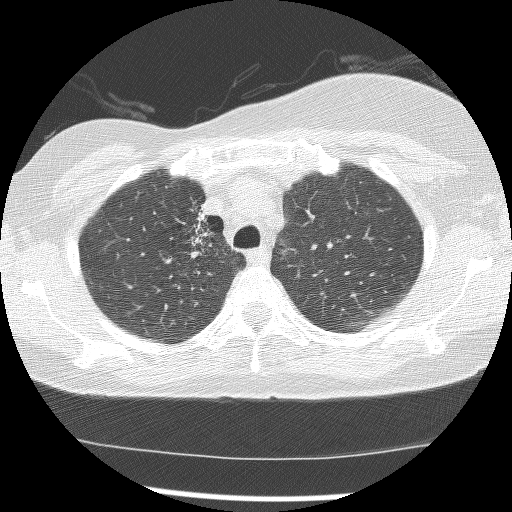
Axial slice from a low-dose chest CT screening exam. Baseline annual screen. Lung window (W 1500 / L -600 HU). Lung (sharp) reconstruction kernel (BONE). Slice 36 of 172 in the series. 512 × 512 image matrix, field of view 315 × 315 mm. Female participant, aged 56 years at enrolment. Current smoker at enrolment.
• Expert-annotated lung lesion, box from (x=165, y=200) to (x=223, y=275) px.
• The screening reader recorded 2 non-calcified nodules or masses ≥4 mm on this exam (right lower lobe, right middle lobe); which of them this box marks is not recorded.